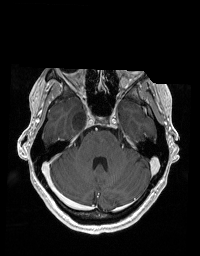
Brain MRI from a brain-tumour surgery series, one axial slice; T1-weighted post-contrast; 1 mm slice thickness; 200 × 256 image matrix. Case-level facts recorded for this patient, not image findings: histopathology: Glioblastoma; WHO grade: 2; IDH mutation: no; tumour location: Right Skull Base Temporal.
Structures marked on this image (outlined manually by an expert reader):
- tumour: bounding box (x1, y1, x2, y2) in pixels: (72, 108, 86, 131)